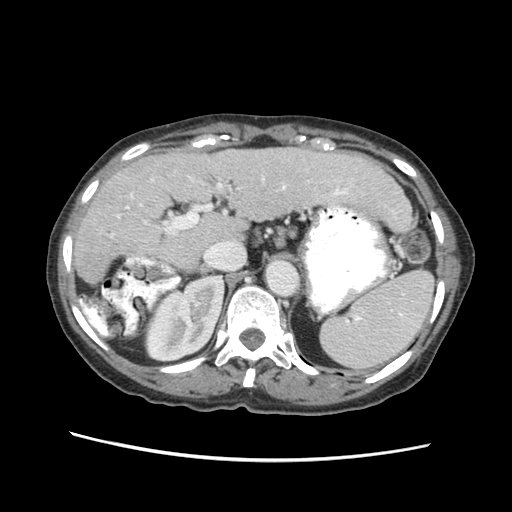
Contrast-enhanced abdominal CT (liver protocol), one axial slice; position 37 of 63 along the scan axis; 120 kVp; soft-tissue window (W 400 / L 40 HU); 2.5 mm slice thickness; 512 × 512 image matrix, field of view 340 × 340 mm. Case-level facts recorded for this patient, not image findings: diagnosis: hepatocellular carcinoma (patient treated with transarterial chemoembolisation; whether this scan precedes or follows treatment is not stated here); TNM stage (as recorded): Stage-I; Child-Pugh class: B.
Annotated regions visible in this slice (semi-automatically segmented with operator editing):
- abdominal aorta: bounding box (x1, y1, x2, y2) in pixels: (267, 260, 297, 295)
- liver parenchyma outside the tumour (the mass and vessels are separate outlines, so this box may not span the whole liver): (74, 144, 408, 282)
- liver vessels: (125, 175, 351, 214)